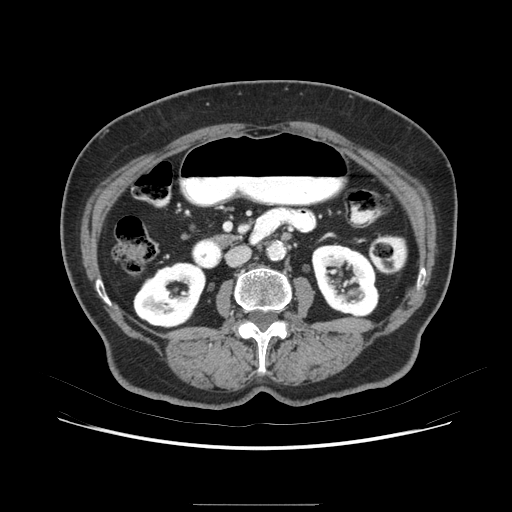
Contrast-enhanced abdominal CT (liver protocol), one axial slice. Slice 17 of 79 in the series (ordered by position). Soft-tissue window (W 400 / L 40 HU). 2.5 mm slice thickness. 512 × 512 image matrix, field of view 380 × 380 mm. Case-level facts recorded for this patient, not image findings: diagnosis: hepatocellular carcinoma (patient treated with transarterial chemoembolisation; whether this scan precedes or follows treatment is not stated here); TNM stage (as recorded): Stage-I; Child-Pugh class: A; tumour differentiation: poorly differentiated; tumour nodularity: uninodular.
Annotated regions visible in this slice (semi-automatic segmentation, software-assisted and operator-edited):
- liver parenchyma outside the tumour (the mass and vessels are separate outlines, so this box may not span the whole liver): bounding box <100,204,118,254> (left, top, right, bottom; pixels)